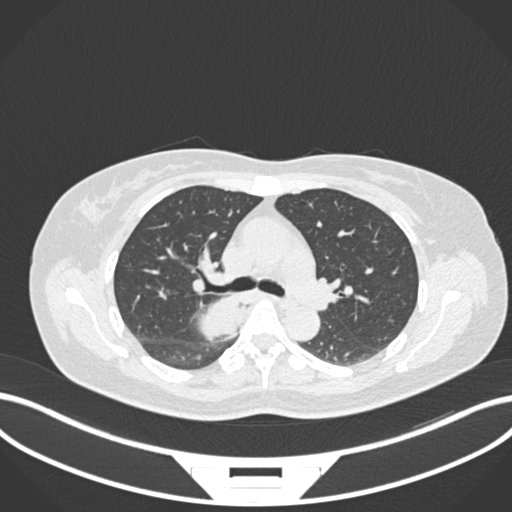
Chest CT, one axial slice; reconstruction kernel B30f; 120 kVp; lung window (W 1500 / L -600 HU); 1 mm slice thickness; 512 × 512 image matrix. Patient: female, 54 years. From the clinical record (not read from this slice): clinical TNM (as recorded): T4 N0 M0.
Outlined on this slice (rectangle marked by the reading radiologist):
- lung tumour (recorded histology: adenocarcinoma): bounding box (x1, y1, x2, y2) in pixels: (192, 288, 254, 343)